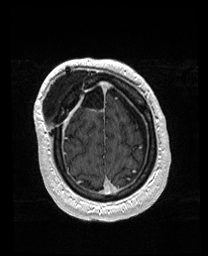
Brain MRI from a brain-tumour surgery series, one axial slice. Position 38 of 176 along the scan axis. T1-weighted post-contrast. 1 mm slice thickness. 208 × 256 image matrix, field of view 208 × 256 mm. From the clinical record (not read from this slice): histopathology: Astrocytoma; WHO grade: 4; IDH mutation: yes; tumour location: Right Orbitofrontal Anterior Temporal Insular.
Annotated regions visible in this slice (expert manual segmentation):
- previous resection cavity: box from (x=64, y=82) to (x=86, y=108) px